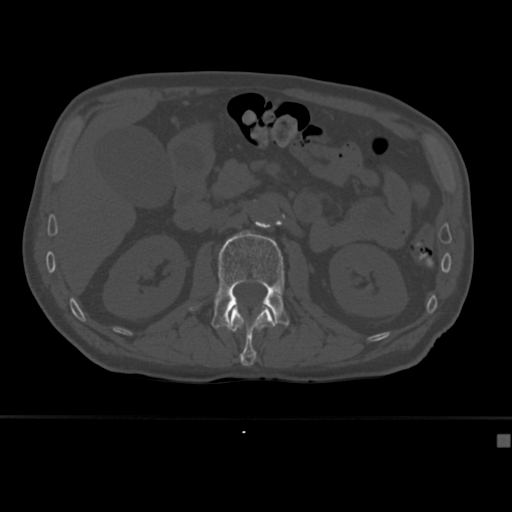
CT including the spine, one axial slice; 120 kVp; bone window (W 1800 / L 400 HU); 1.5 mm slice thickness; 512 × 512 image matrix, field of view 337 × 337 mm. Male patient, age 64 years. Case-level facts recorded for this patient, not image findings: primary cancer: uterus.
Structures marked on this image (semi-automatically segmented with operator editing):
- L1 vertebra: bounding box (x1, y1, x2, y2) in pixels: (229, 306, 276, 366)
- L2 vertebra: (189, 230, 289, 331)